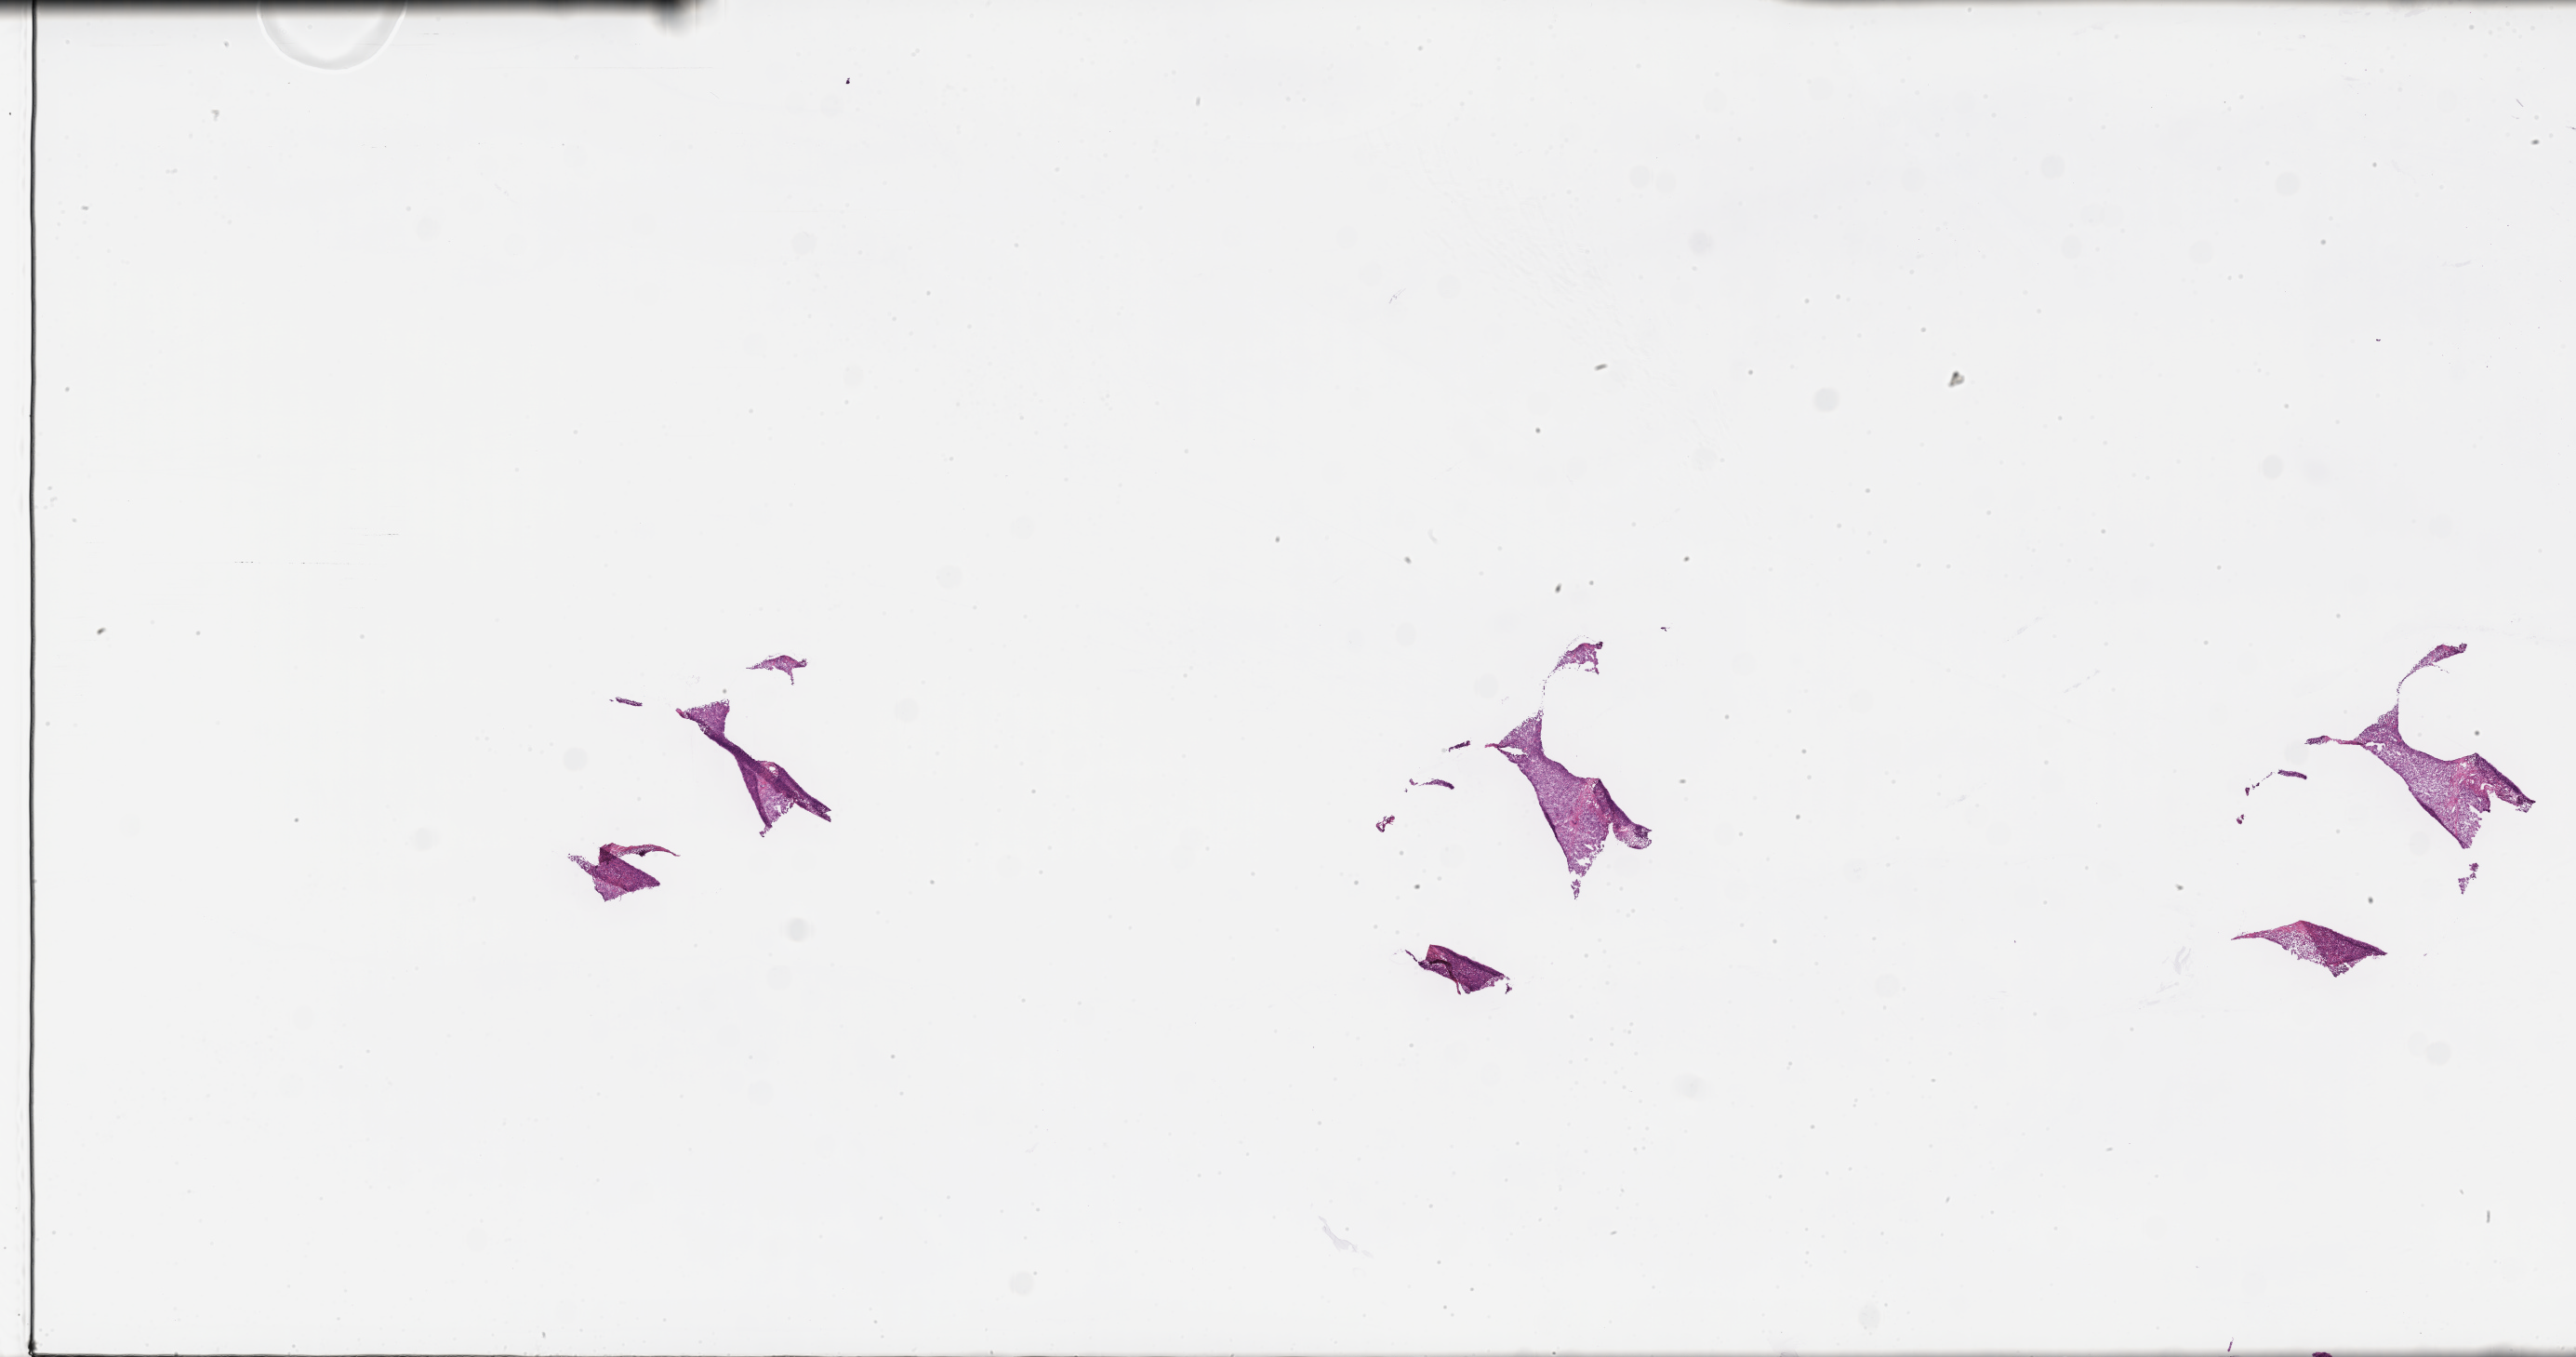
Whole-slide image, haematoxylin and eosin stain, shown as a low-resolution overview of the whole scanned area (about 44.7 x 23.5 mm), cryosection, specimen: primary tumor, site: breast (left). Patient: female, age at initial diagnosis 83 years. Pathologist review of this section (percent, as recorded): tumor cells 80%, tumor nuclei 80%, stromal cells 10%, necrosis 0%, normal cells 10%. Inflammatory infiltration, as recorded: lymphocyte infiltration 10%, monocyte infiltration 0%, neutrophil infiltration 0%.
Section: bottom of the tissue portion. Histologic diagnosis: Lobular carcinoma, NOS.